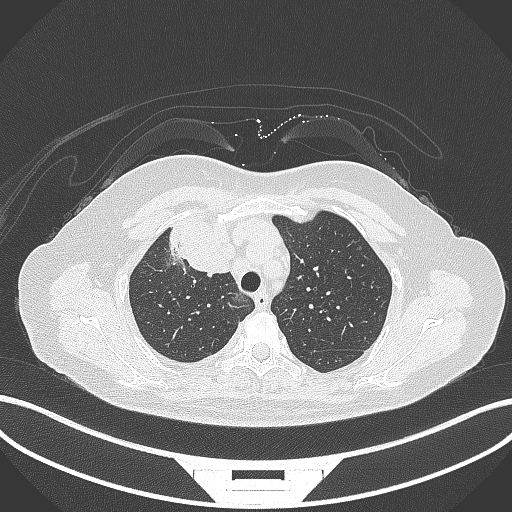
Chest CT, one axial slice; position 235 of 305 along the scan axis; reconstruction kernel B70f; lung window (W 1500 / L -600 HU); 512 × 512 image matrix, field of view 400 × 400 mm. Female patient, age 52 years. From the clinical record (not read from this slice): clinical TNM (as recorded): T3 N1 M1.
Annotated regions visible in this slice (bounding box drawn by a radiologist):
- lung tumour (recorded histology: adenocarcinoma): bounding box <165,213,234,279> (left, top, right, bottom; pixels)